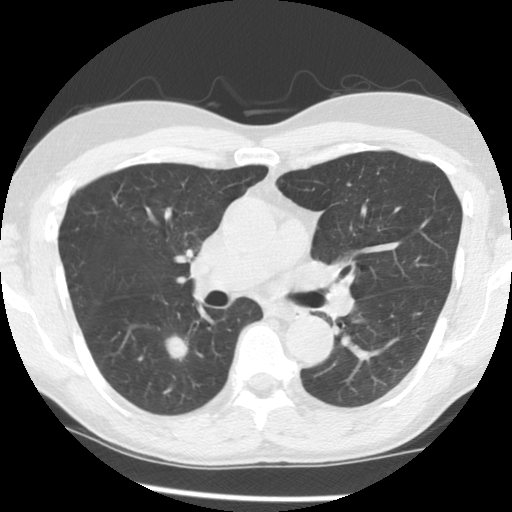
Low-dose screening chest CT, one axial slice. Position 82 of 145 along the scan axis. Lung window (W 1500 / L -600 HU). 2.5 mm slice thickness. 512 × 512 image matrix, field of view 320 × 320 mm.
Annotated regions visible in this slice (outlined manually by an expert reader):
- lesion 1 (tumor, lower lobe of right lung): box from (x=165, y=335) to (x=188, y=361) px